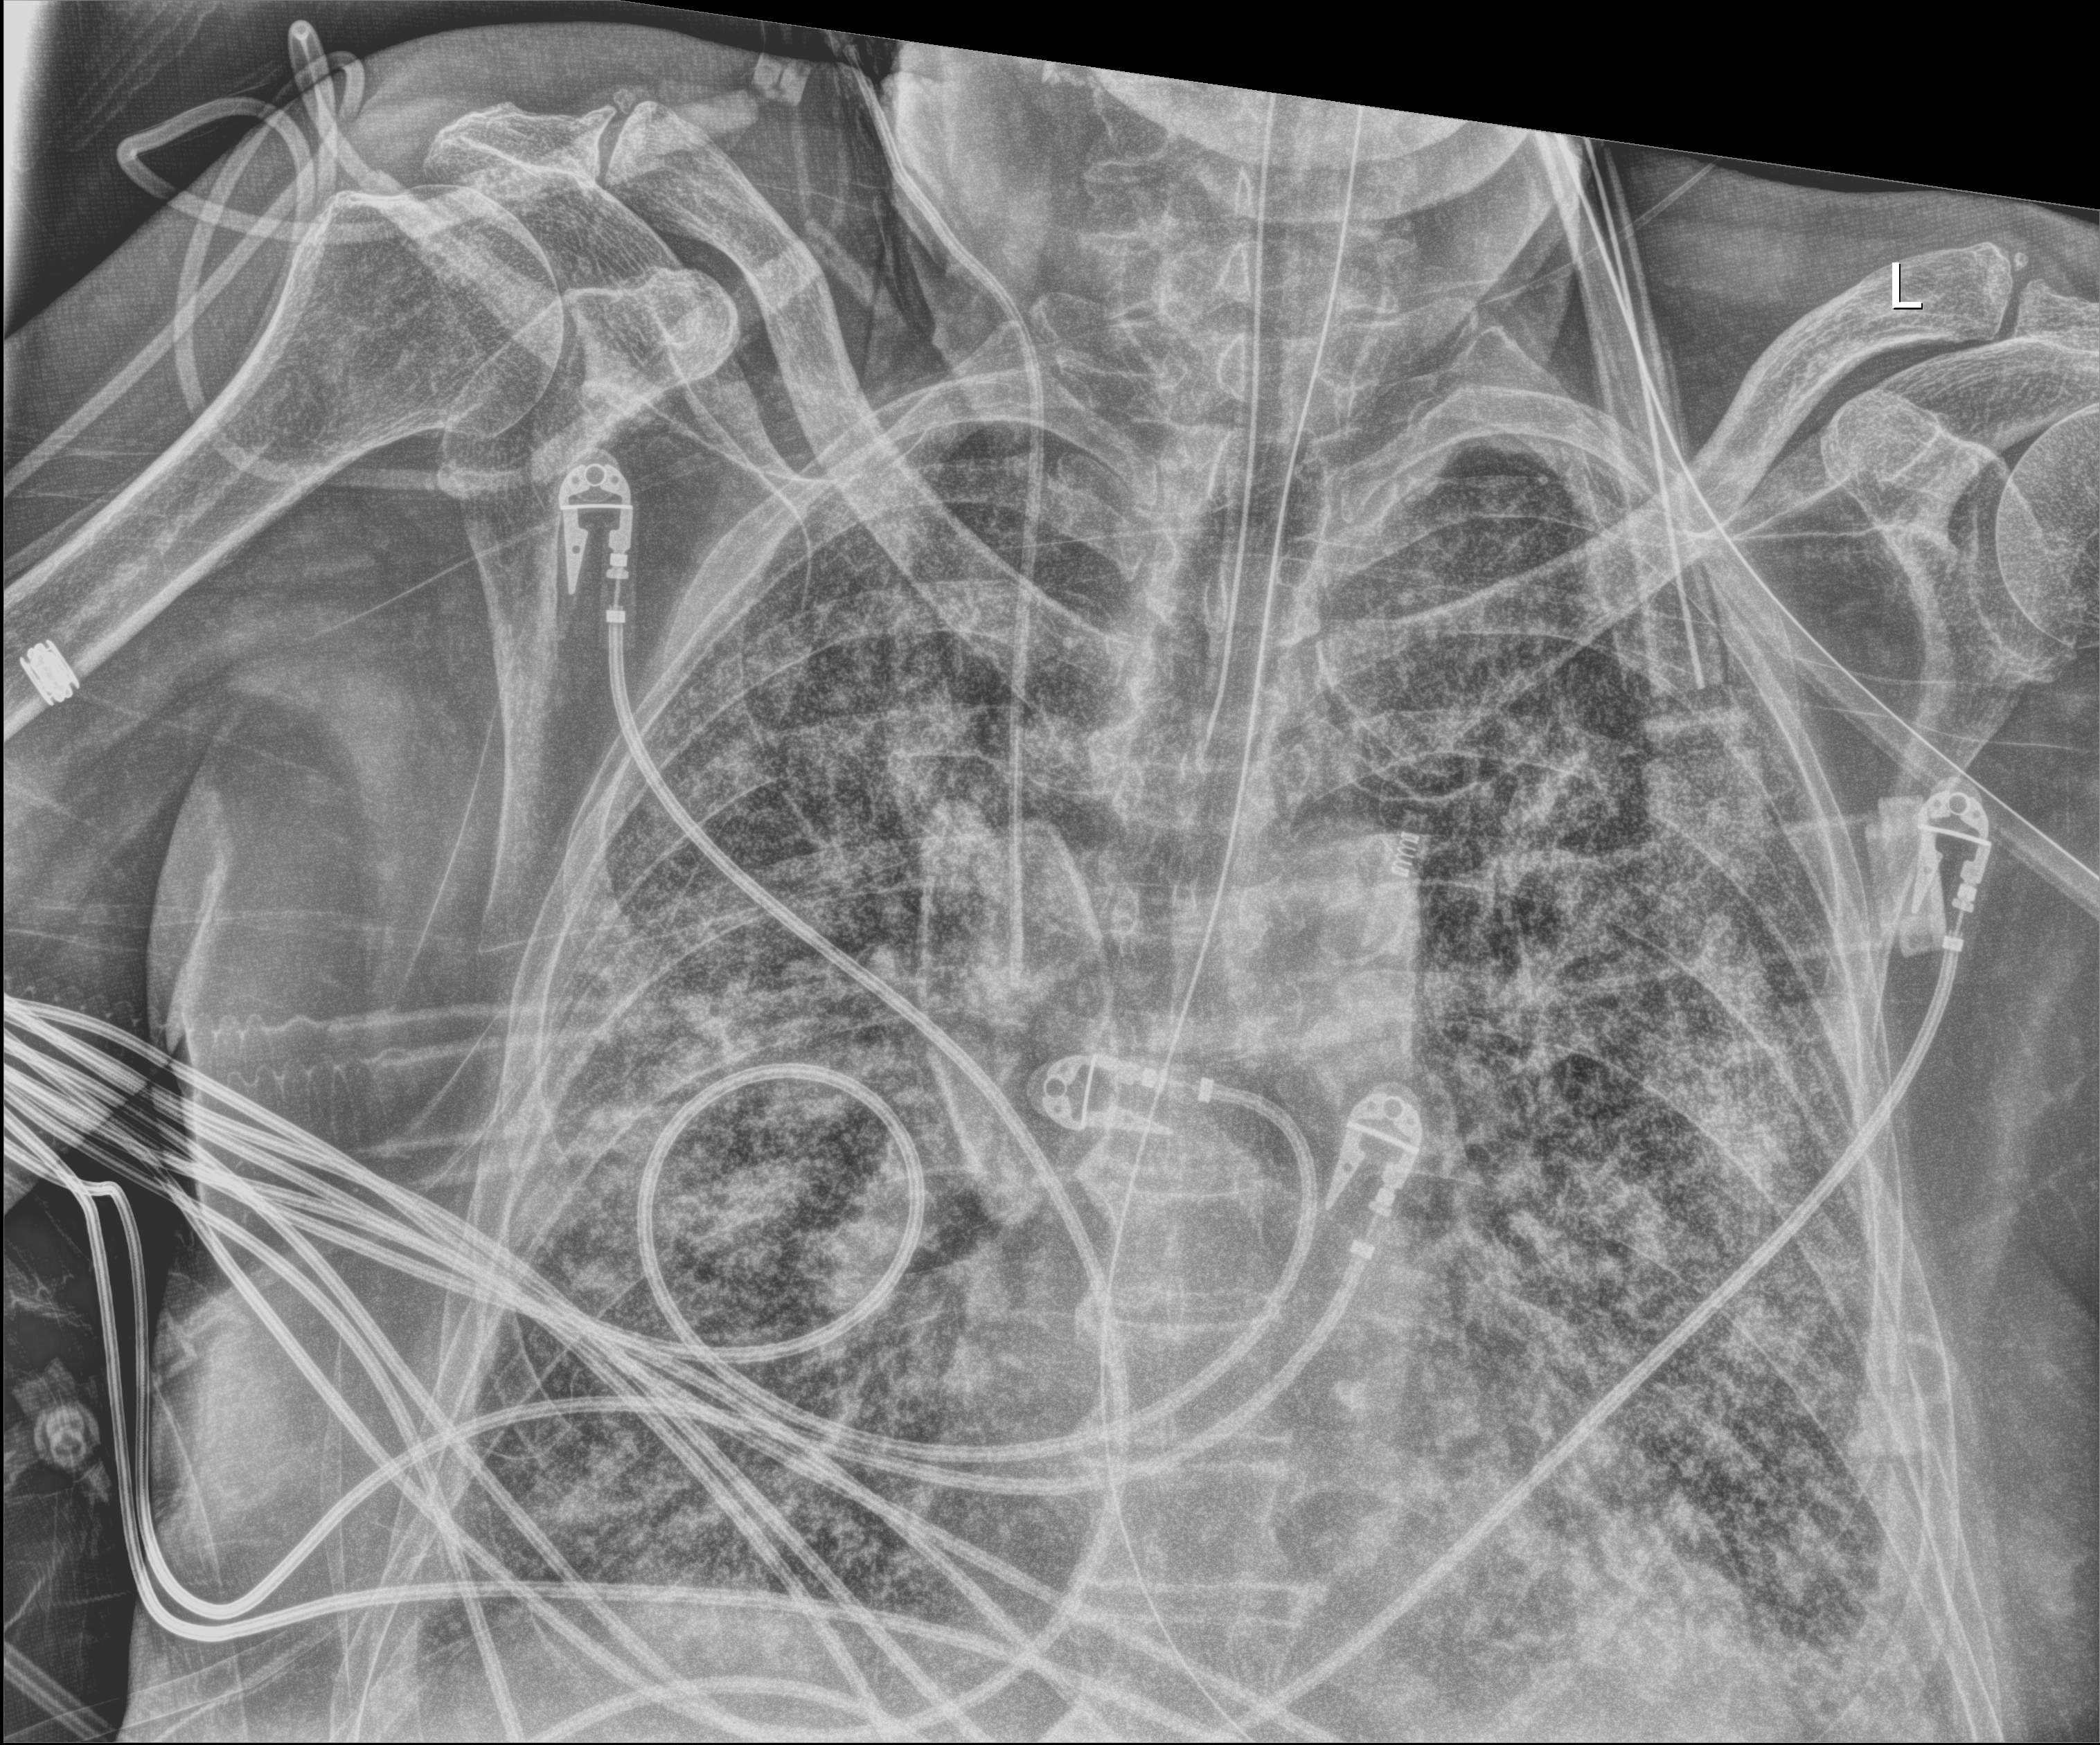
Bedside chest radiograph (digital radiography); anteroposterior (AP) projection. Patient hospitalised with COVID-19; male, aged 75–90 years.
Hospital-stay facts (about this admission, not read from this image; timing relative to this image not recorded): mechanically ventilated during this hospital stay: yes.